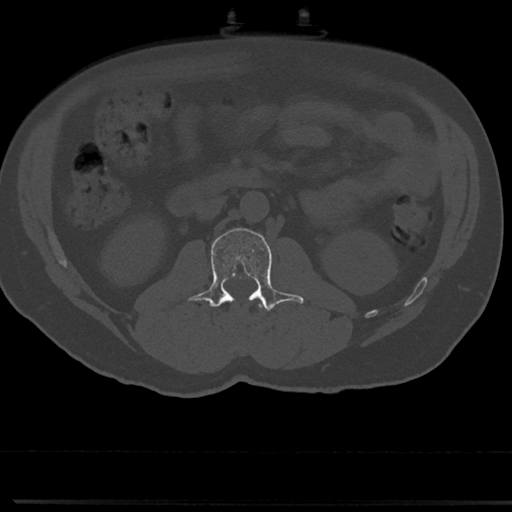
CT including the spine, one axial slice. Position 20 of 817 along the scan axis. Reconstruction kernel Br40s/3. 120 kVp. Bone window (W 1800 / L 400 HU). 512 × 512 image matrix. Patient: male, 61 years. Case-level facts recorded for this patient, not image findings: primary cancer: prostate.
Outlined on this slice (semi-automatic segmentation, software-assisted and operator-edited):
- L1 vertebra: box from (x=241, y=302) to (x=262, y=342) px
- L2 vertebra: (x=191, y=228)–(x=304, y=313)